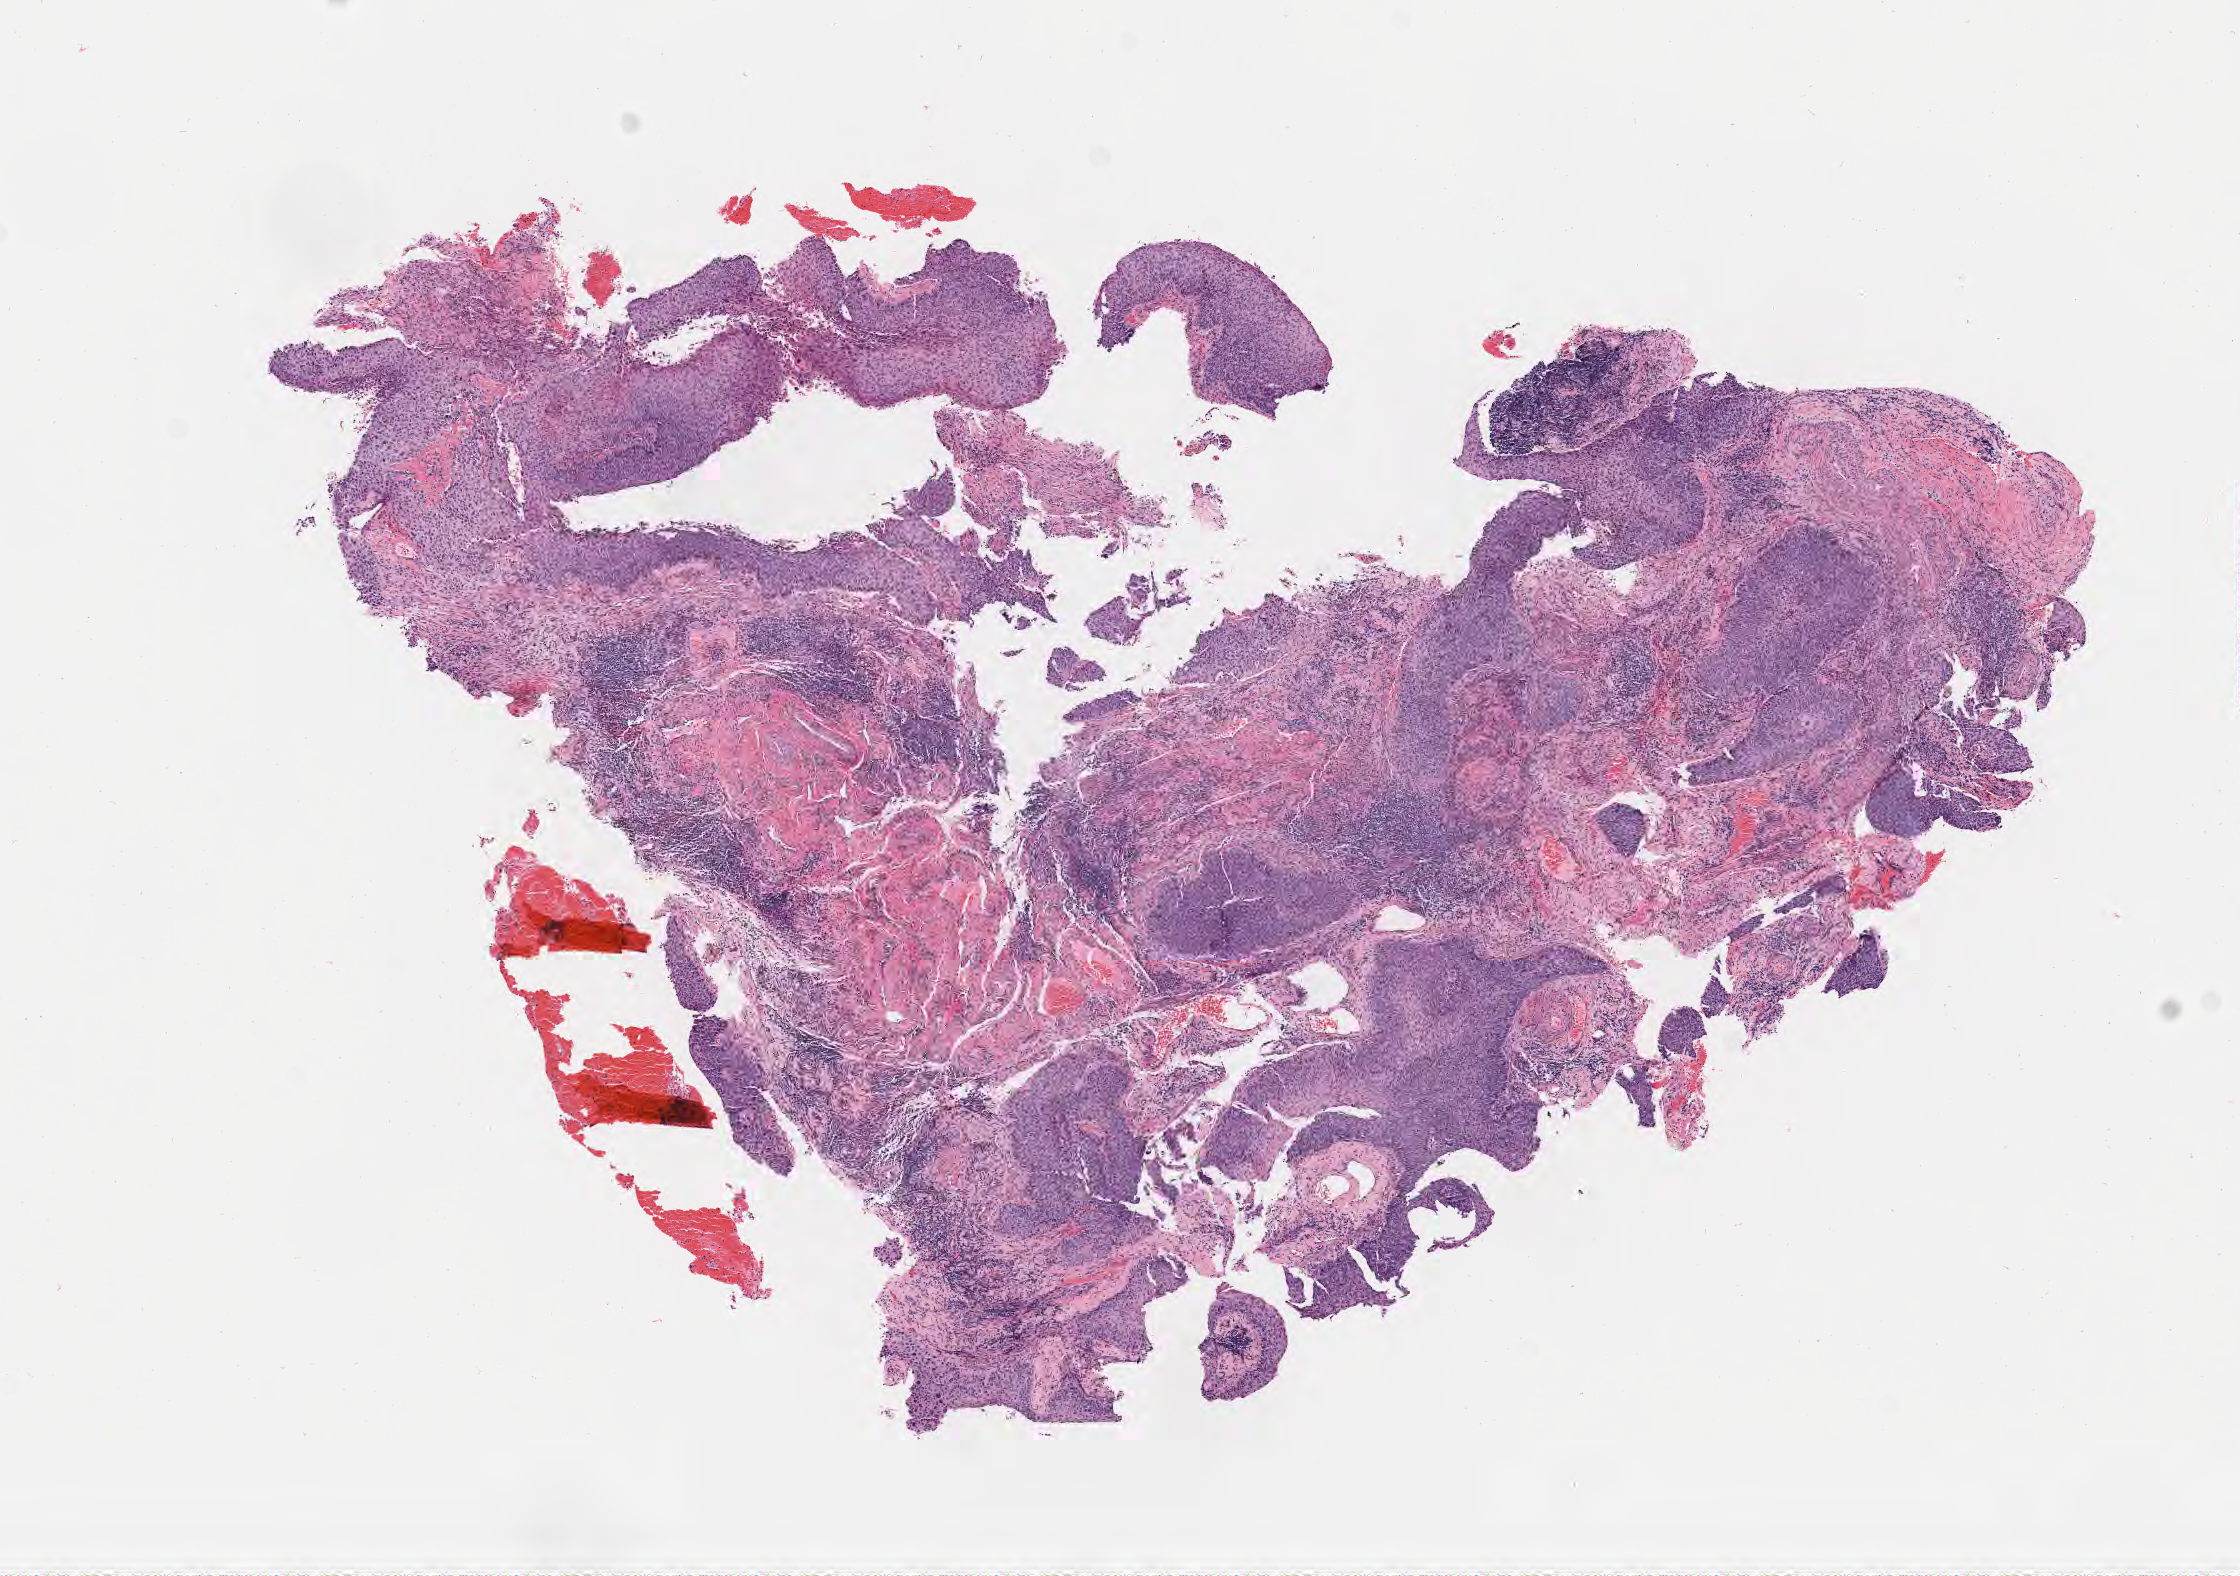
Hematoxylin and eosin (H&E) whole-slide image — low-resolution overview of the scanned area, about 9.1 x 6.4 mm. Tumor tissue. Anatomic site: cervix. Female patient, 50 years old.
Diagnosis: Squamous cell carcinoma, large cell, nonkeratinizing, NOS.